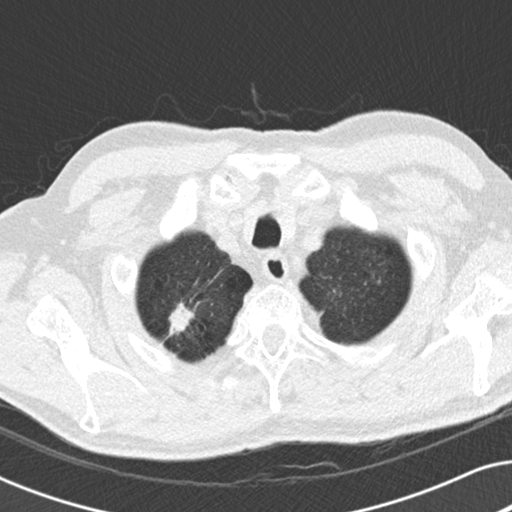
Low-dose screening chest CT, one axial slice. Position 172 of 191 along the scan axis. 120 kVp. Lung window (W 1500 / L -600 HU). 2 mm slice thickness. 512 × 512 image matrix, field of view 330 × 330 mm.
Outlined on this slice (manually delineated by an expert):
- lesion 2 (nodule, lower lobe of right lung): bounding box <169,302,193,335> (left, top, right, bottom; pixels)